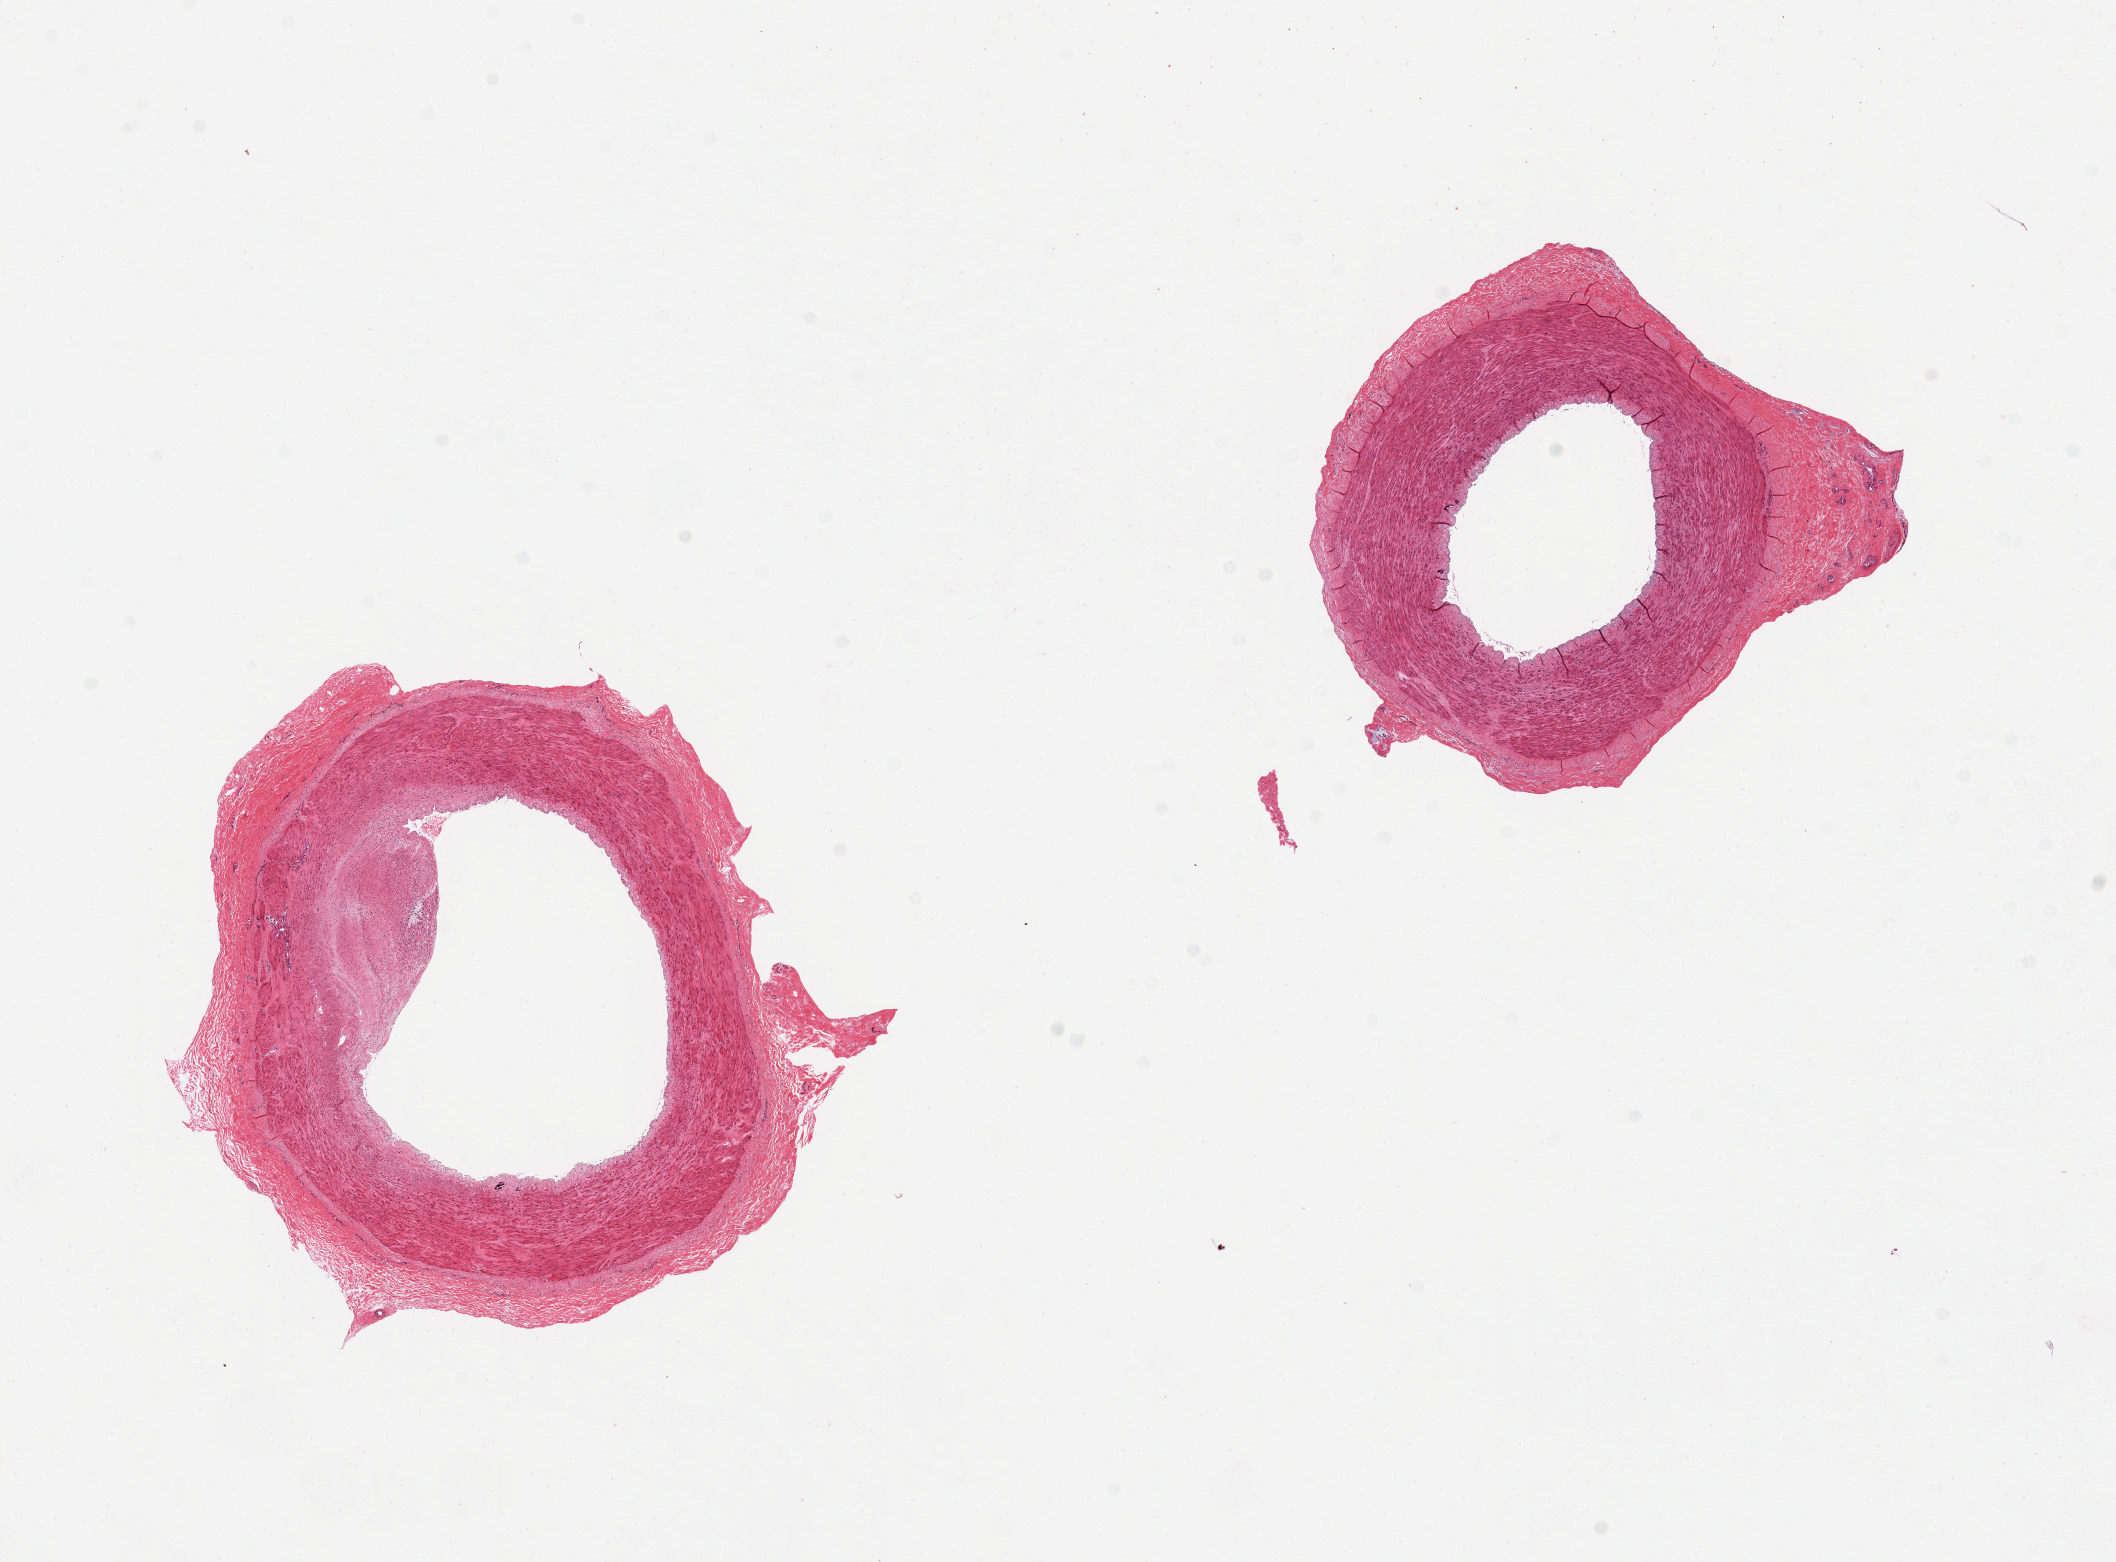
Whole-slide image, H&E stain, whole scanned area (about 16.7 x 12.4 mm, from a 20x scan) shown as a low-resolution overview, PAXgene-fixed, paraffin-embedded tissue, sampled site (target tissue): tibial artery, donor tissue sample. Donor sex: male.
• review note (as recorded): 2 pieces; well trimmed